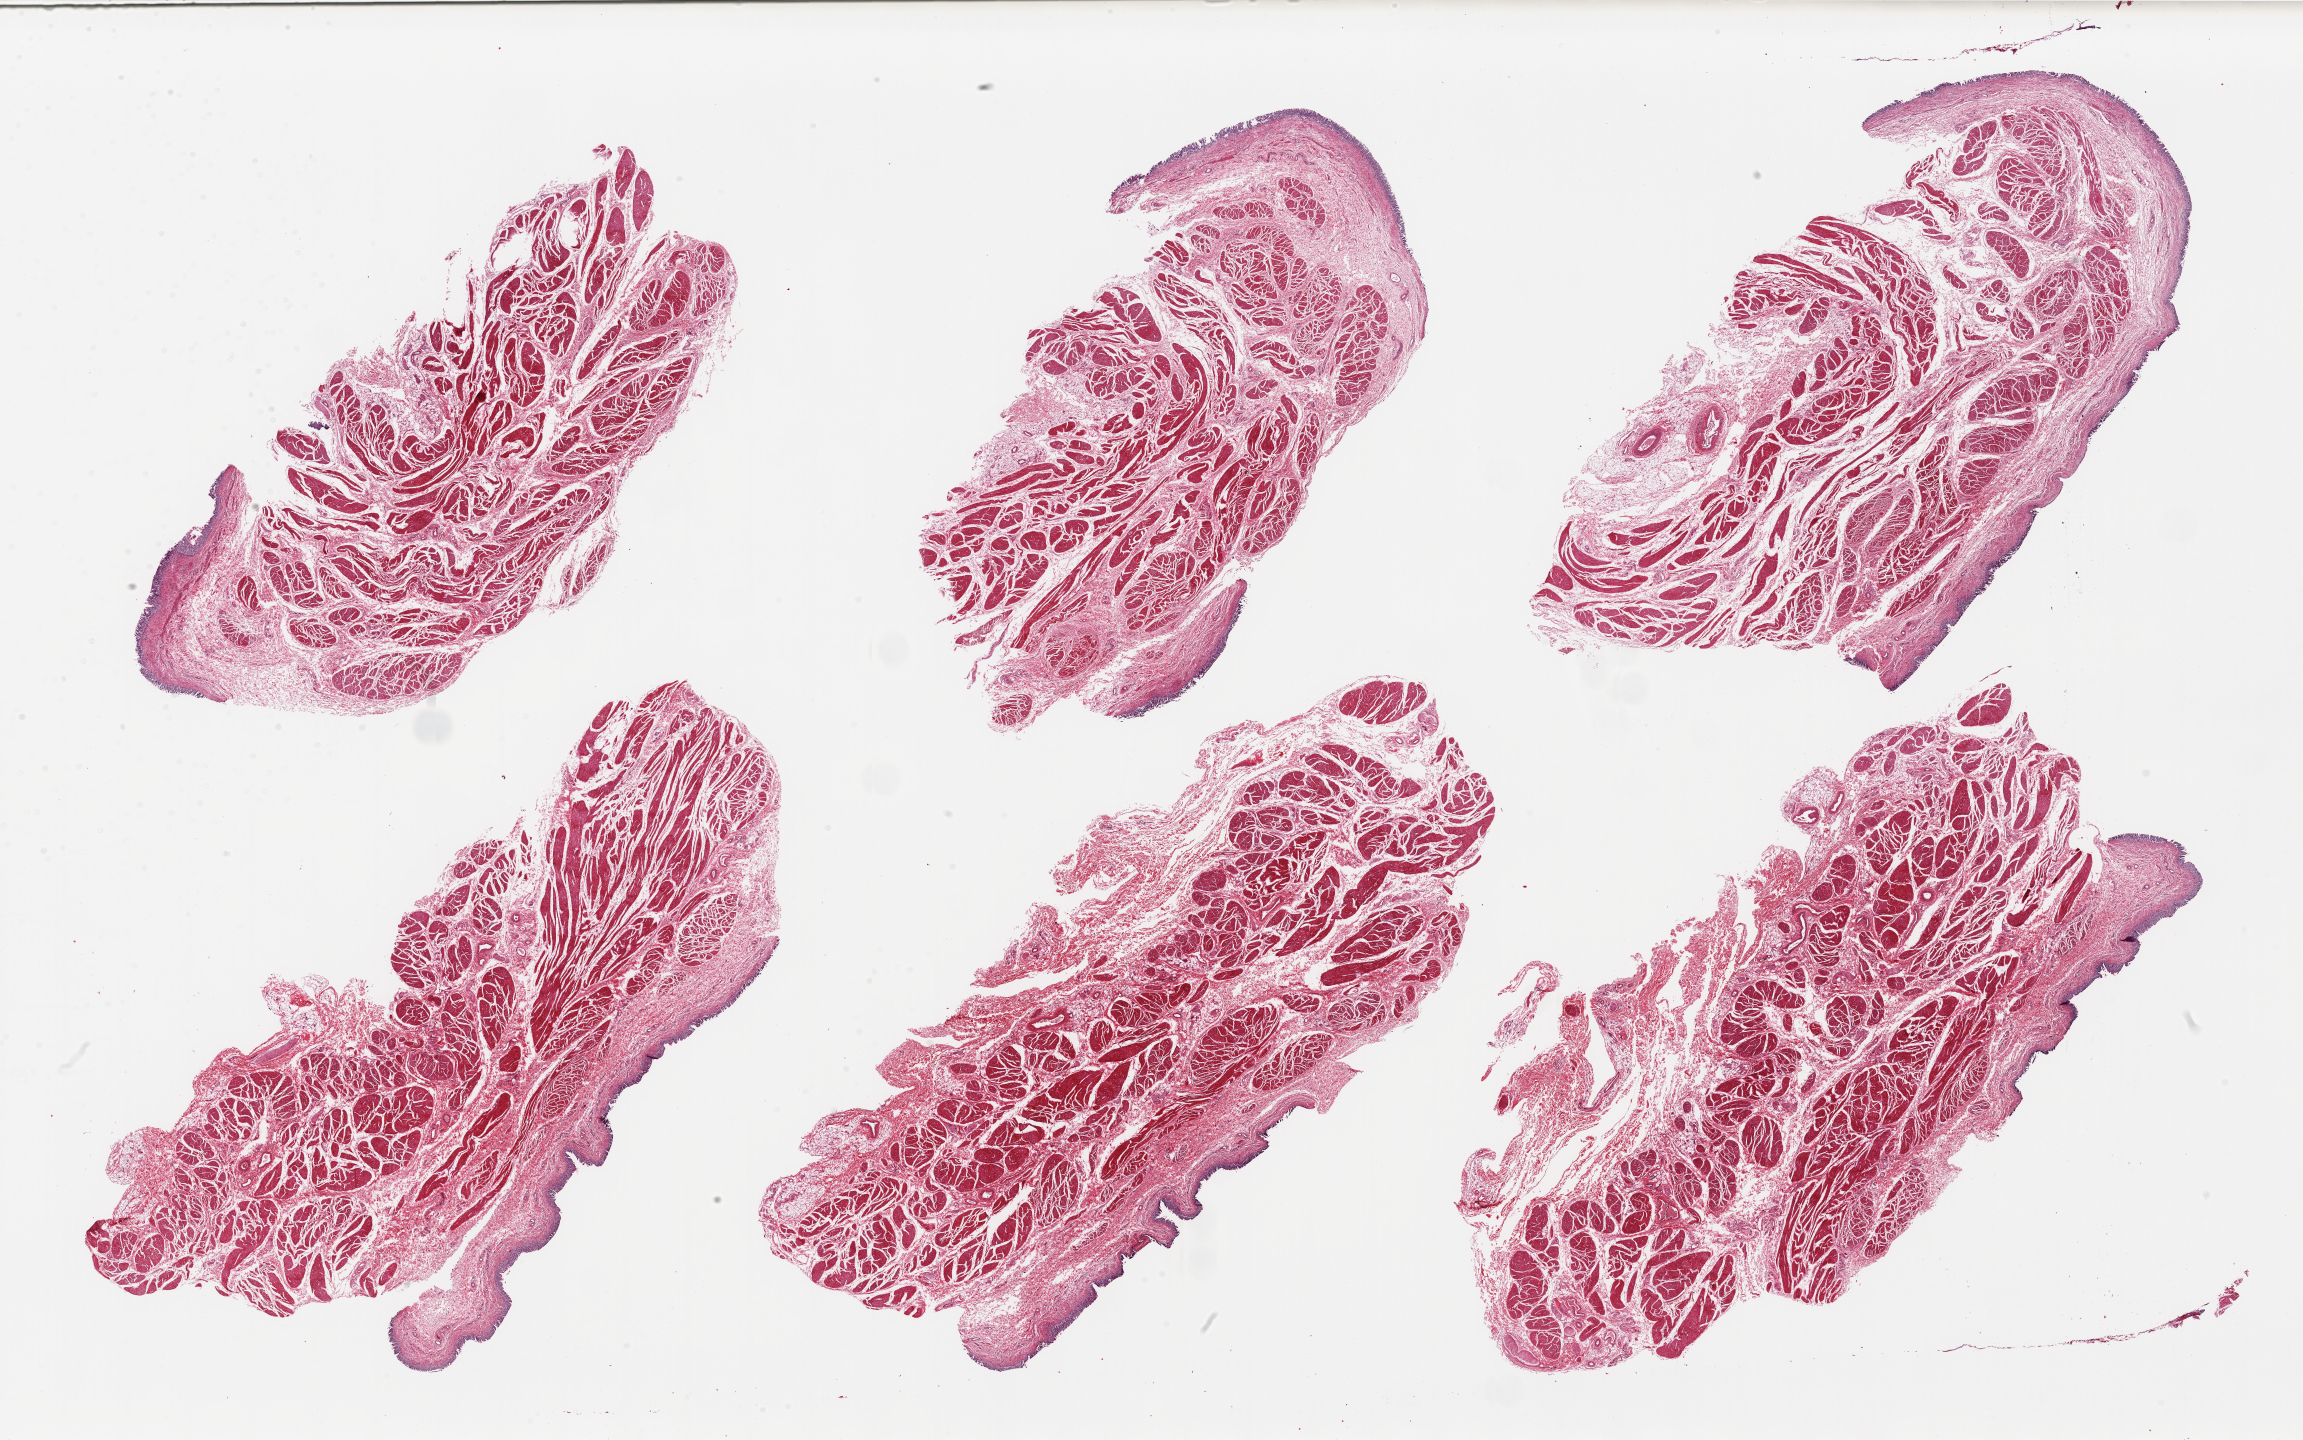
Hematoxylin and eosin (H&E) whole-slide image — shown as a low-resolution overview of the whole scanned area (about 36.4 x 22.8 mm); PAXgene-fixed, paraffin-embedded tissue; section of vagina (target tissue); donor tissue sample.
Pathologist's review note for this sample: 2 pieces; bladder, not vagina.